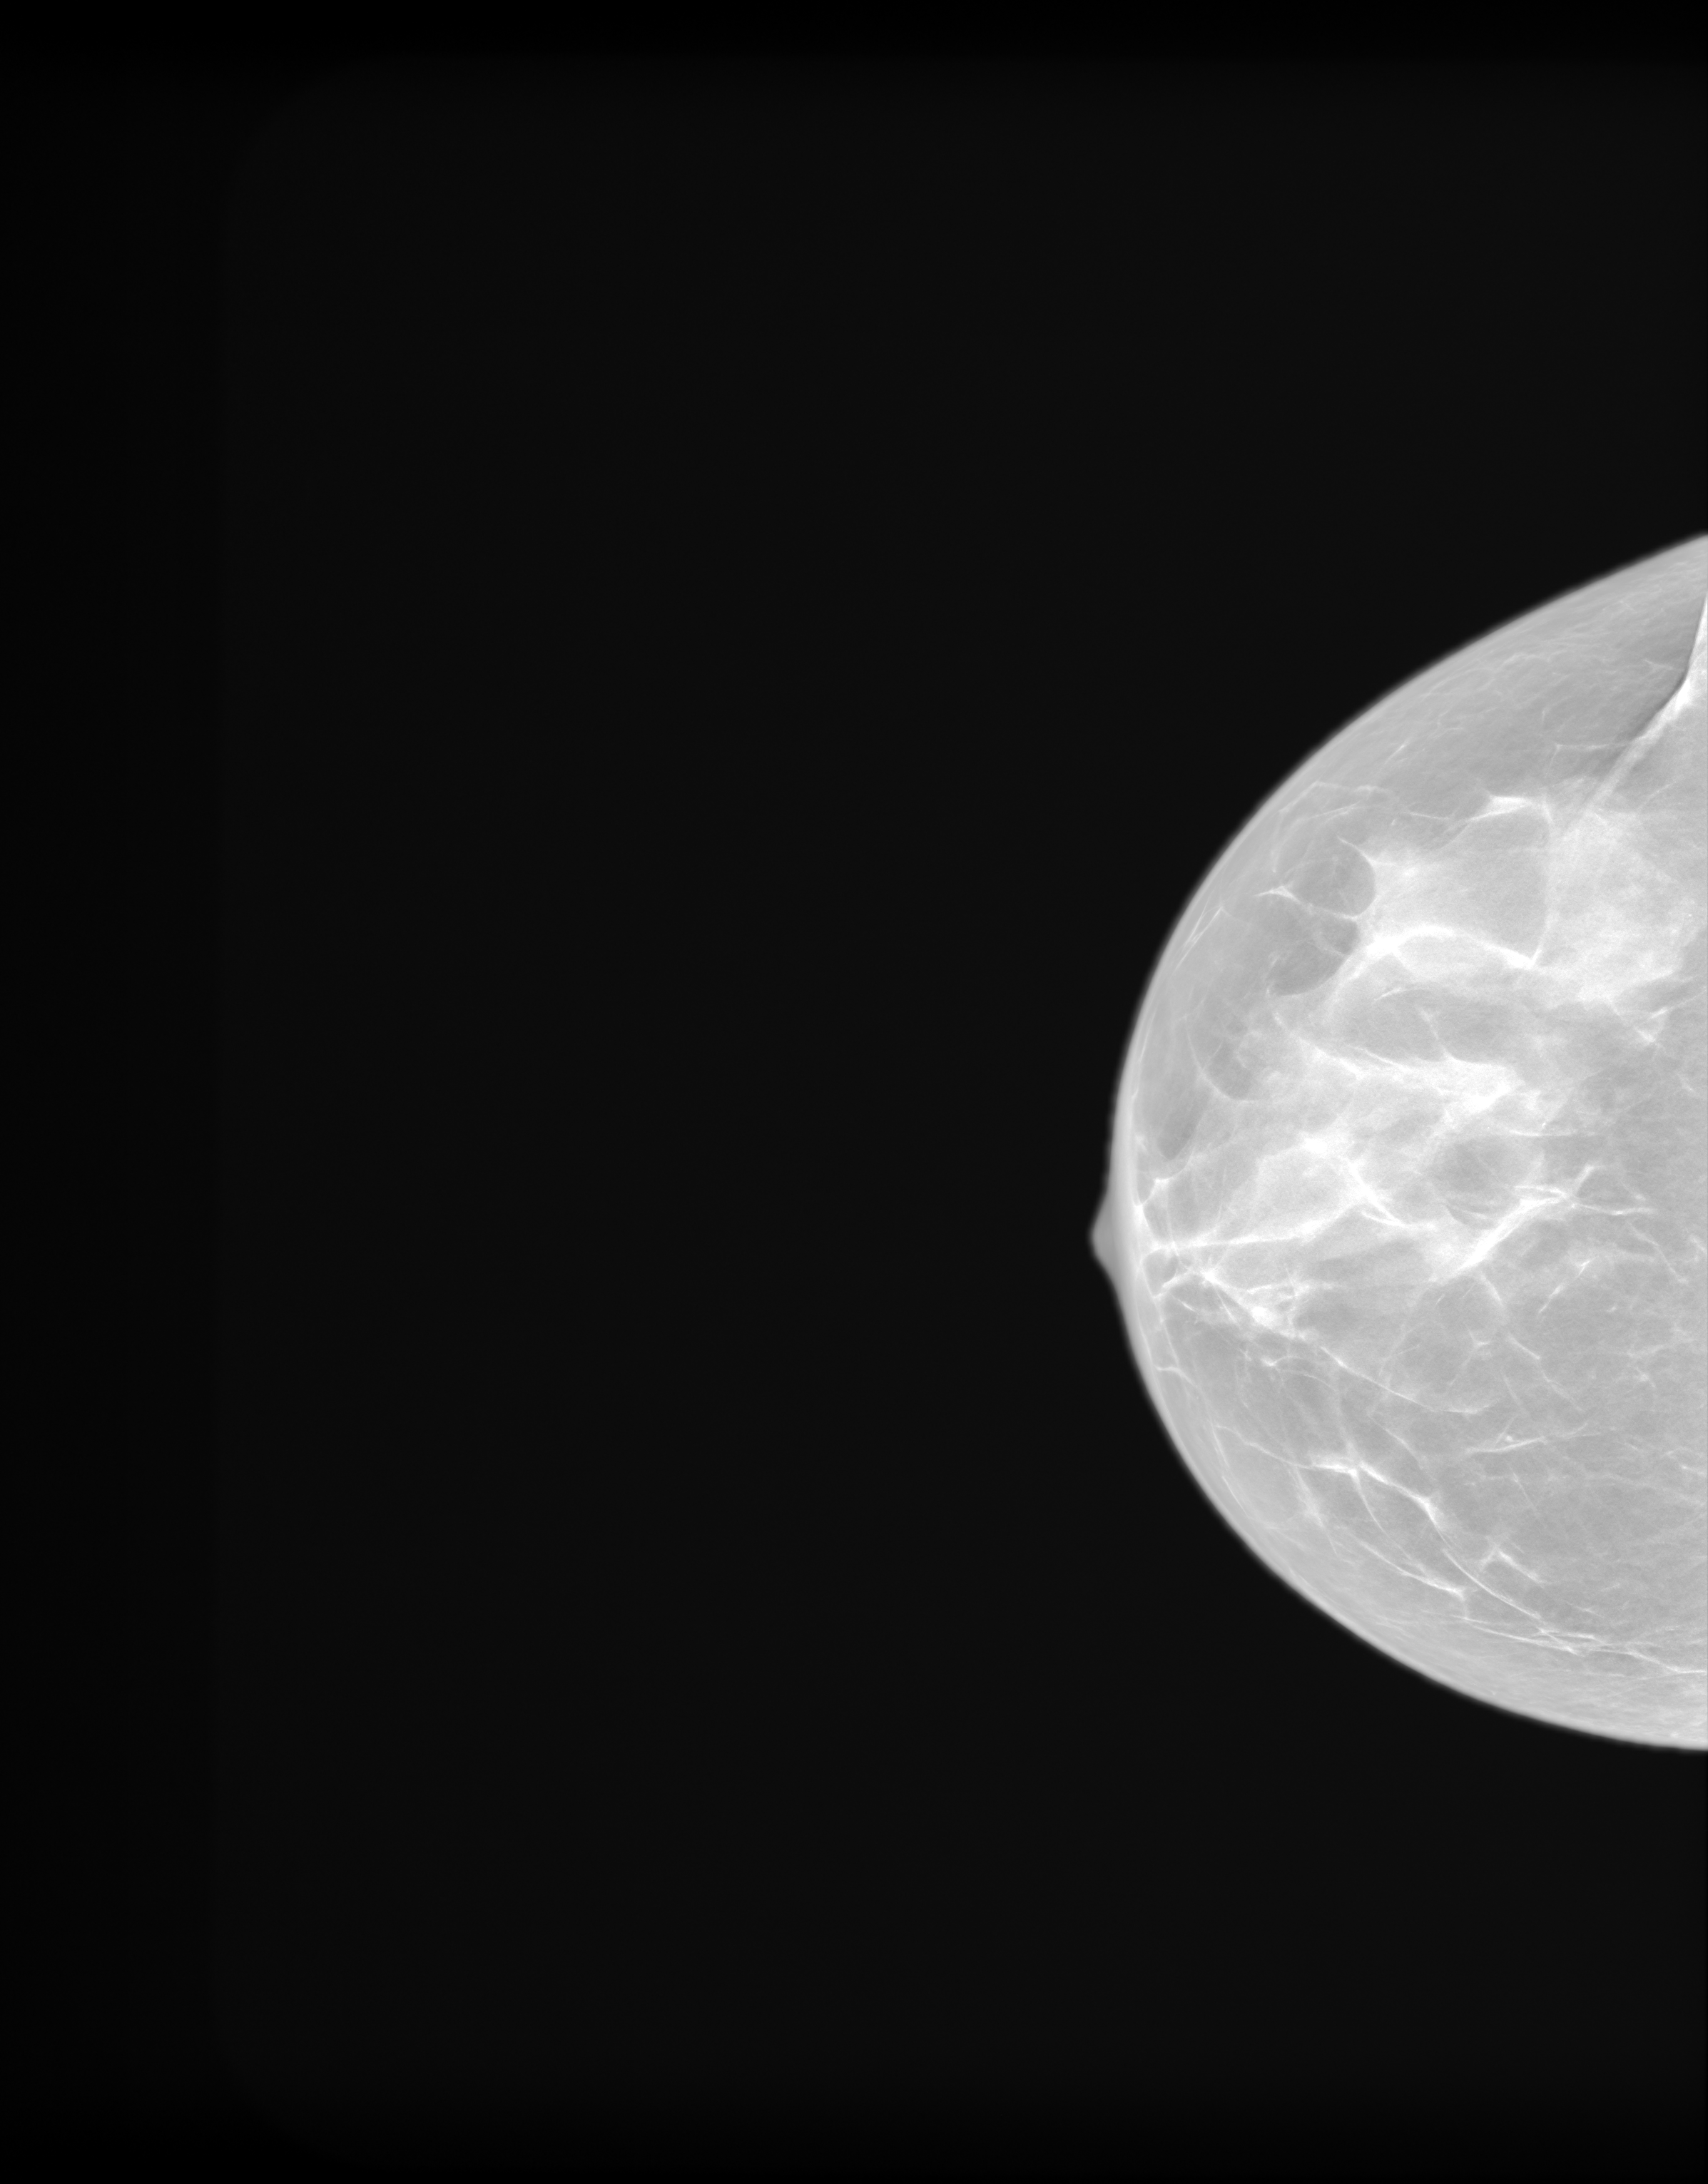
Annual screening mammography examination, system: SenoIris_1SP2(440). Patient: female, 52 years.
Image type: synthesized 2-D view from tomosynthesis. Breast: right. Projection: CC view.